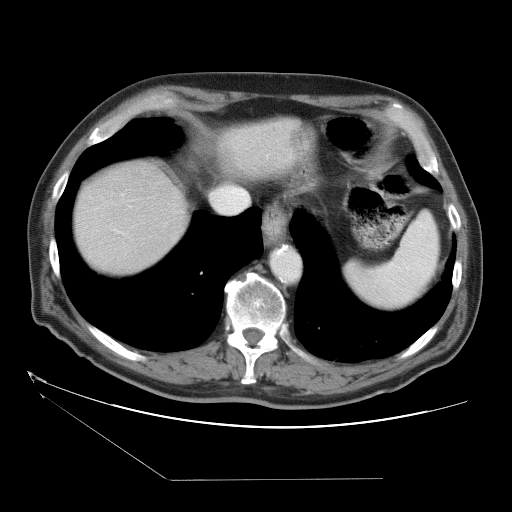
Contrast-enhanced abdominal CT (liver protocol), one axial slice; position 31 of 38 along the scan axis; 120 kVp; one of 2 acquisitions stored at this slice position; soft-tissue window (W 400 / L 40 HU); 512 × 512 image matrix. From the clinical record (not read from this slice): diagnosis: hepatocellular carcinoma (patient treated with transarterial chemoembolisation; whether this scan precedes or follows treatment is not stated here); TNM stage (as recorded): Stage-II; Child-Pugh class: A; tumour differentiation: moderately differentiated; tumour nodularity: multinodular.
Annotated regions visible in this slice (semi-automatically segmented with operator editing):
- liver parenchyma outside the tumour (the mass and vessels are separate outlines, so this box may not span the whole liver): bounding box [x1, y1, x2, y2] px = [74, 118, 304, 272]
- liver vessels: [112, 229, 123, 234]